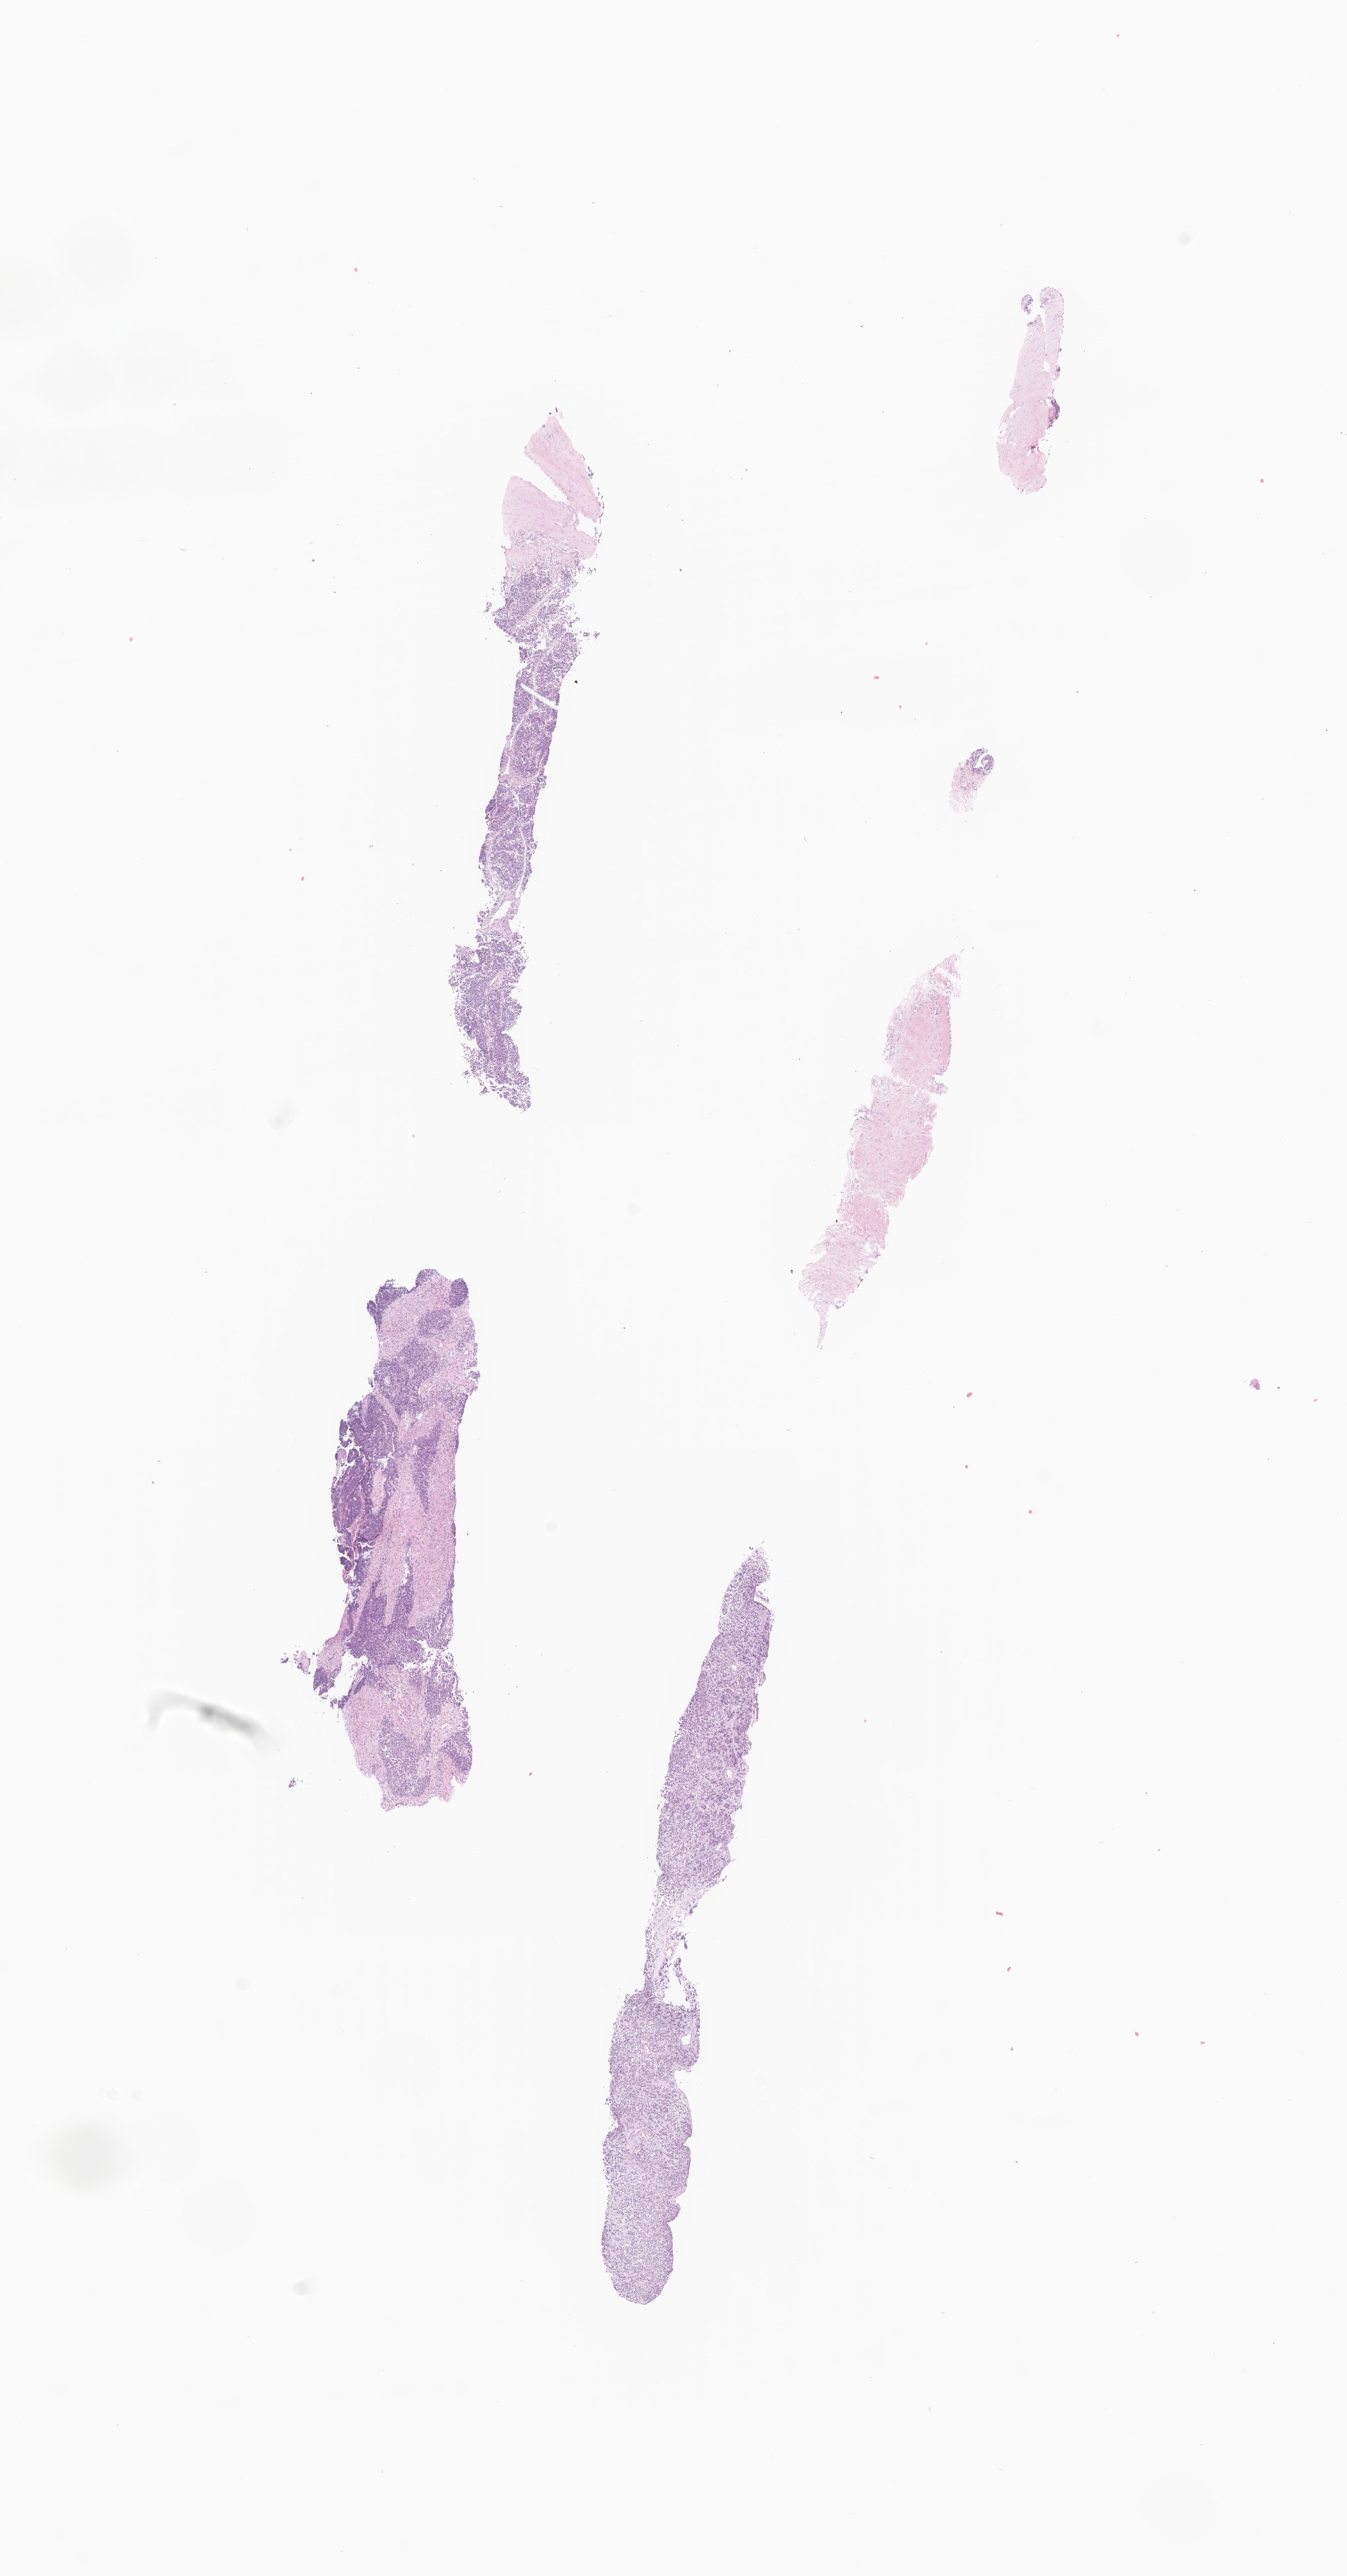
Digitized haematoxylin and eosin-stained section of tumor tissue from the retroperitoneum — whole scanned area (about 8.9 x 16.9 mm) shown as a low-resolution overview, formalin-fixed, paraffin-embedded (FFPE) tissue. Female patient, age 80 months (6 years 8 months).
Diagnosis: Rhabdomyosarcoma, NOS.